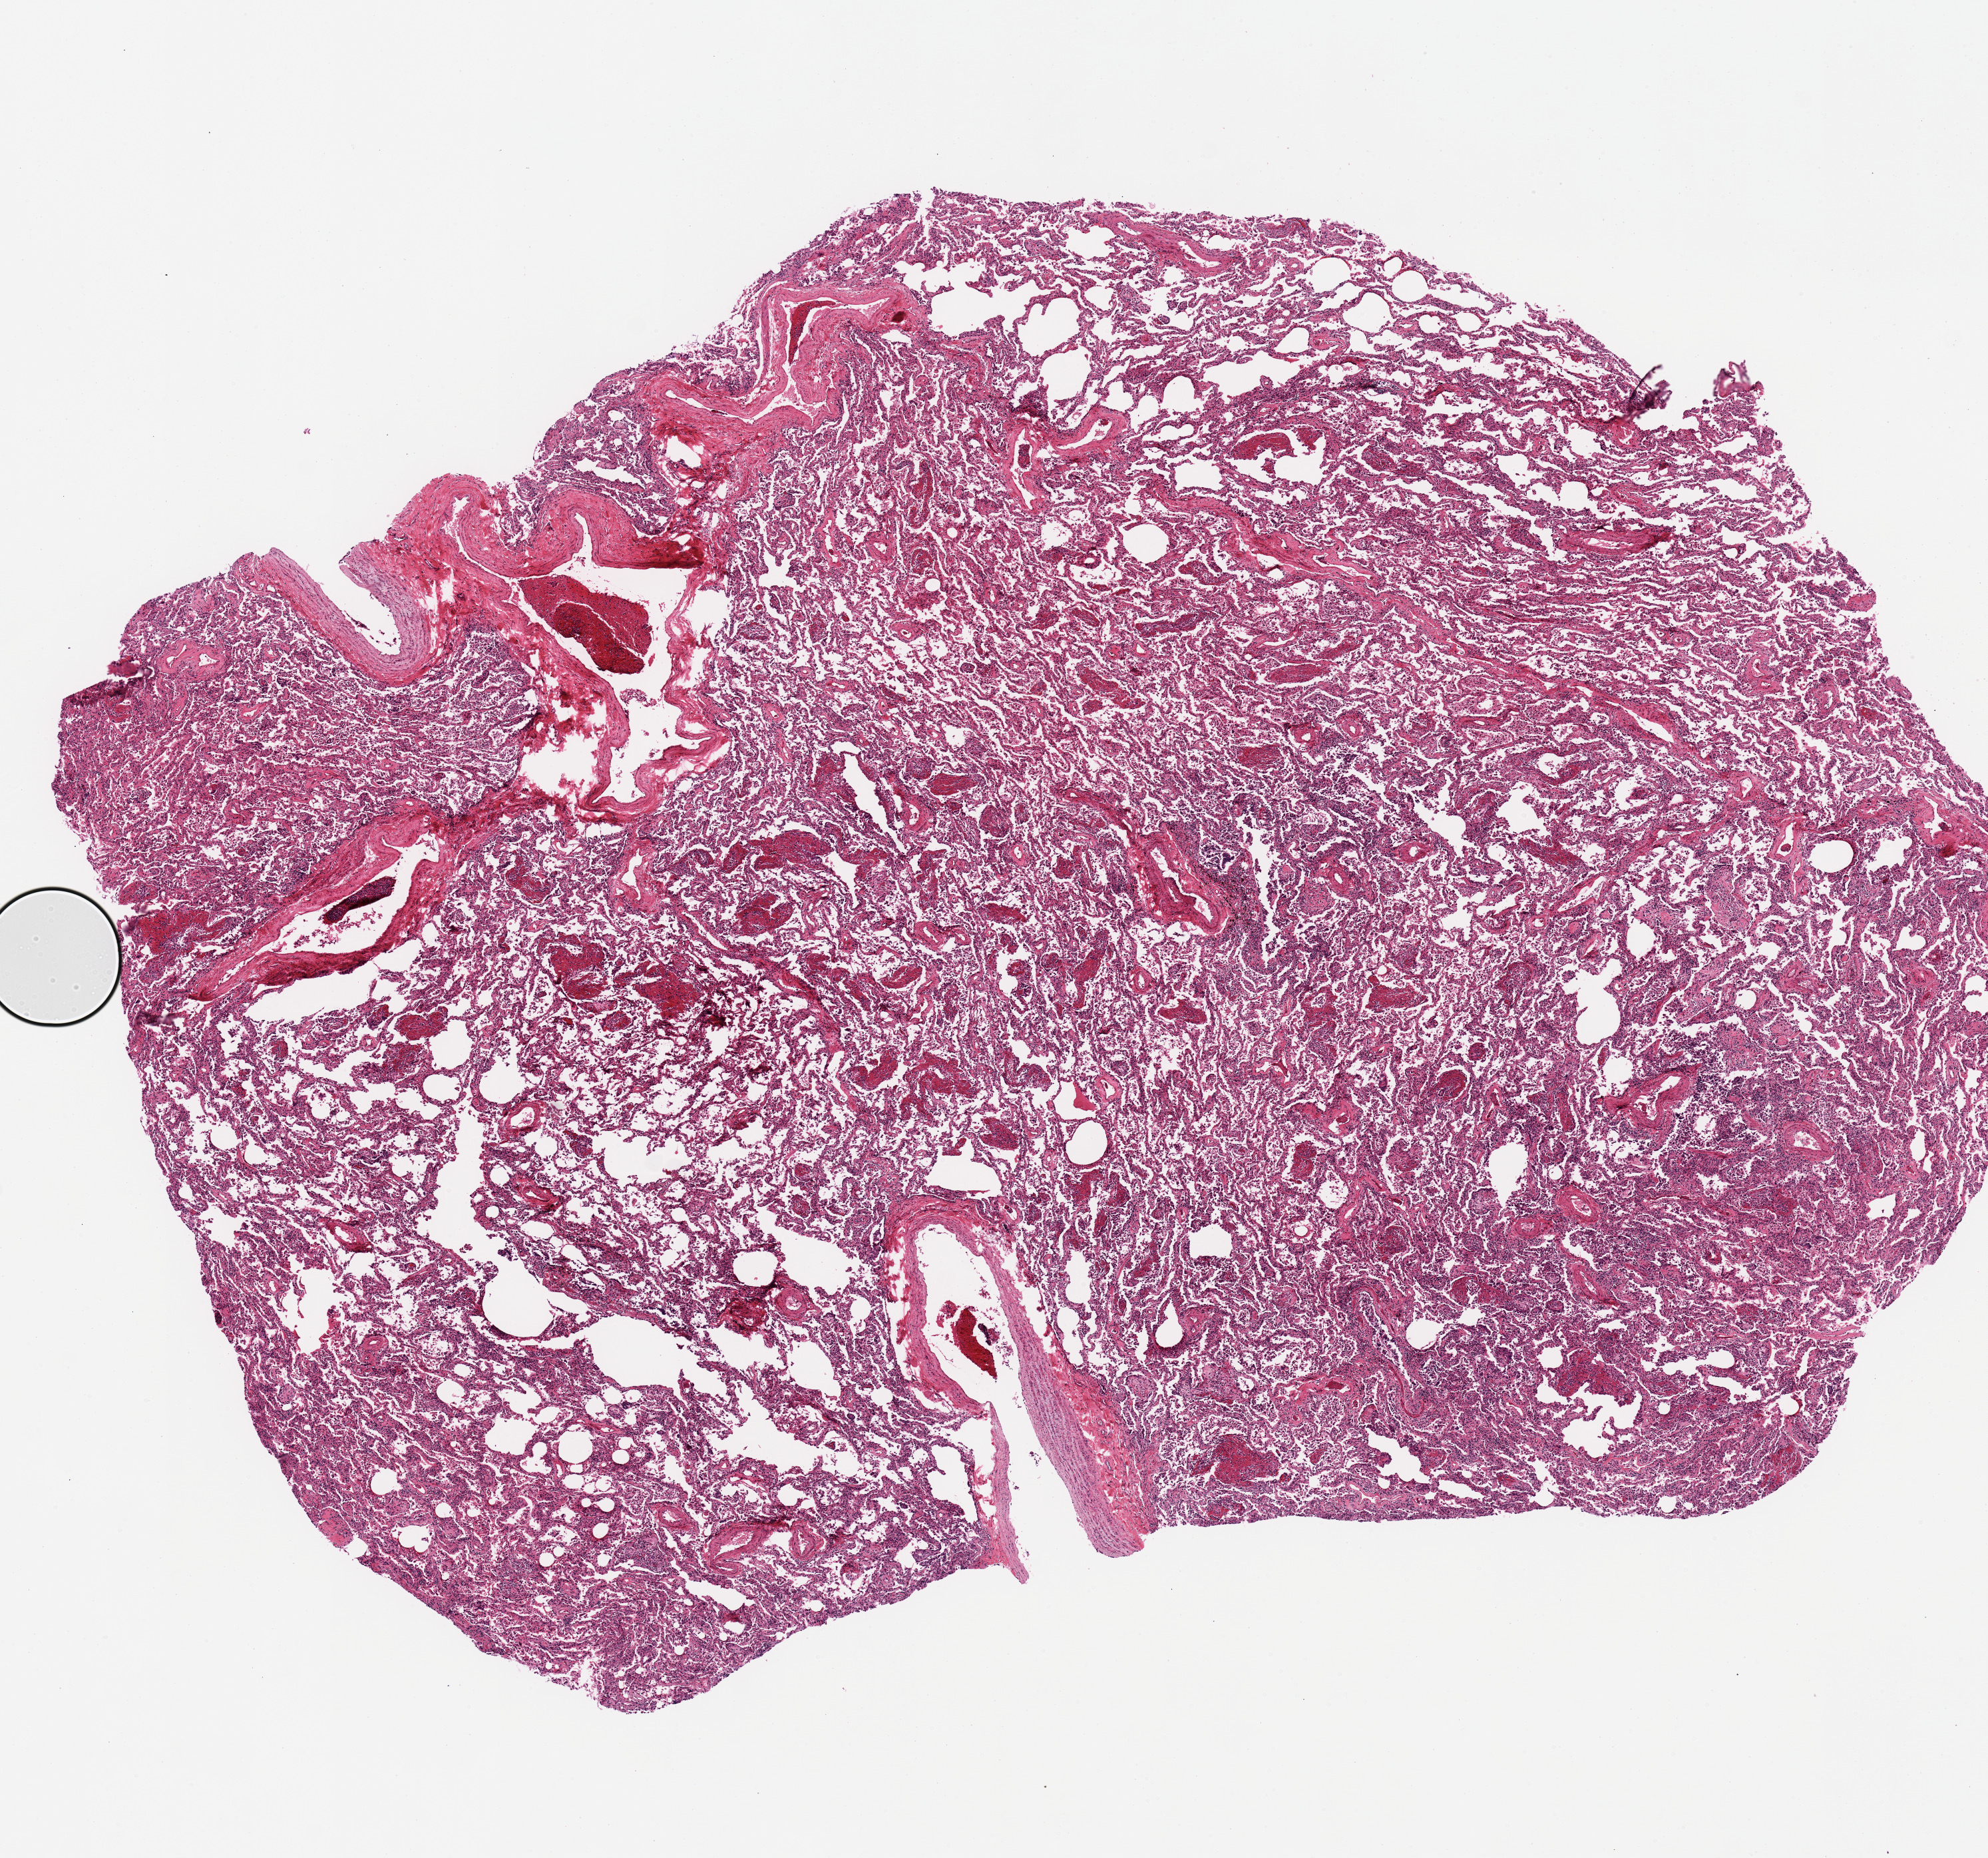
Digitized haematoxylin and eosin-stained section, brightfield, shown as a low-resolution overview of the whole scanned area (about 11.8 x 11.0 mm, acquisition: 20x scan); PAXgene-fixed paraffin-embedded (PFPE) section; section of lung (target tissue); donor tissue sample. Donor: female.
Reviewer comment on this tissue sample: Diffuse chronic (?acute) interstitial pneumonitis???pending glass slide review.